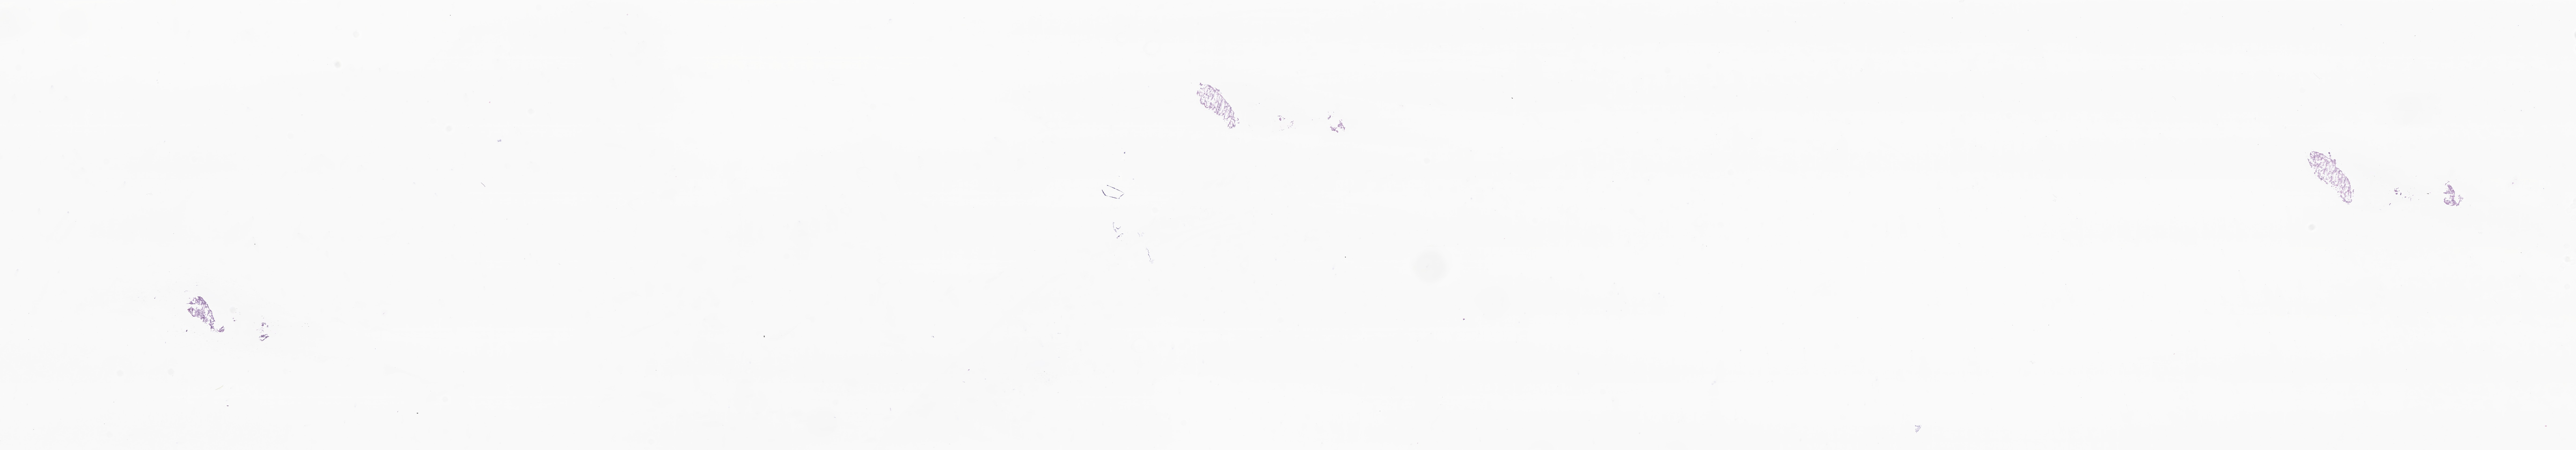
Digitized hematoxylin and eosin (H&E)-stained section of tumor tissue from the brain, a low-resolution overview of the entire scanned area, about 40.5 x 7.1 mm; frozen section (OCT-embedded). Male patient, age 70 months (5 years 10 months).
• diagnosis: Glioma, malignant